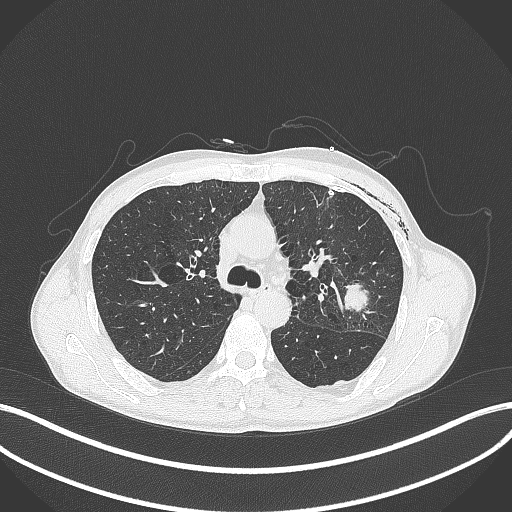
Chest CT, one axial slice. Slice 268 of 457 in the series (ordered by position). Reconstruction kernel B70f. 120 kVp. Lung window (W 1500 / L -600 HU). 1 mm slice thickness. 512 × 512 image matrix, field of view 400 × 400 mm. Male patient, age 58 years. Case-level facts recorded for this patient, not image findings: clinical TNM (as recorded): T3 N0 M0.
Annotated regions visible in this slice (bounding box drawn by a radiologist):
- lung tumour (recorded histology: adenocarcinoma): box from (x=340, y=275) to (x=369, y=312) px